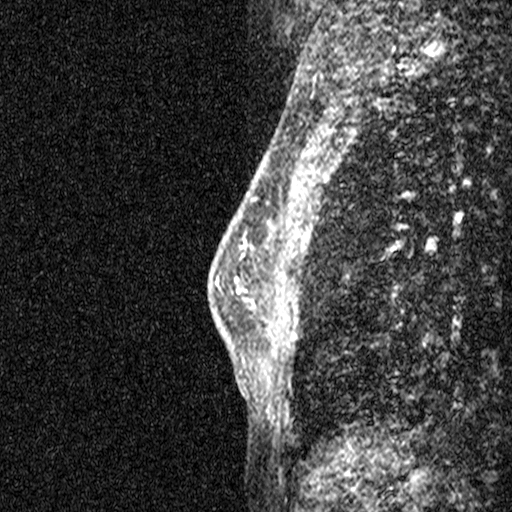
Breast MRI (dynamic contrast-enhanced), one sagittal slice. Slice 24 of 44 in the series (ordered by position). Dynamic contrast-enhanced study with each time point stored as its own series, time point 2 of 3 at this slice position (early post-contrast, ordered by acquisition time). 1.5 T. TE 4.5 ms, TR 11 ms. 512 × 512 image matrix, field of view 200 × 200 mm. Female patient, age 45 years. From the clinical record (not read from this slice): setting: breast cancer imaged before/during neoadjuvant chemotherapy; receptor status: HR-positive, HER2-negative.
Outlined on this slice (semi-automatically segmented with operator editing):
- analysis volume of interest (the breast-tissue region the enhancement analysis was run in; not a lesion): bounding box [x1, y1, x2, y2] px = [256, 218, 351, 359]
- tumour enhancement mask (voxels above the 90 % enhancement threshold inside the analysis volume of interest): [294, 316, 297, 324]